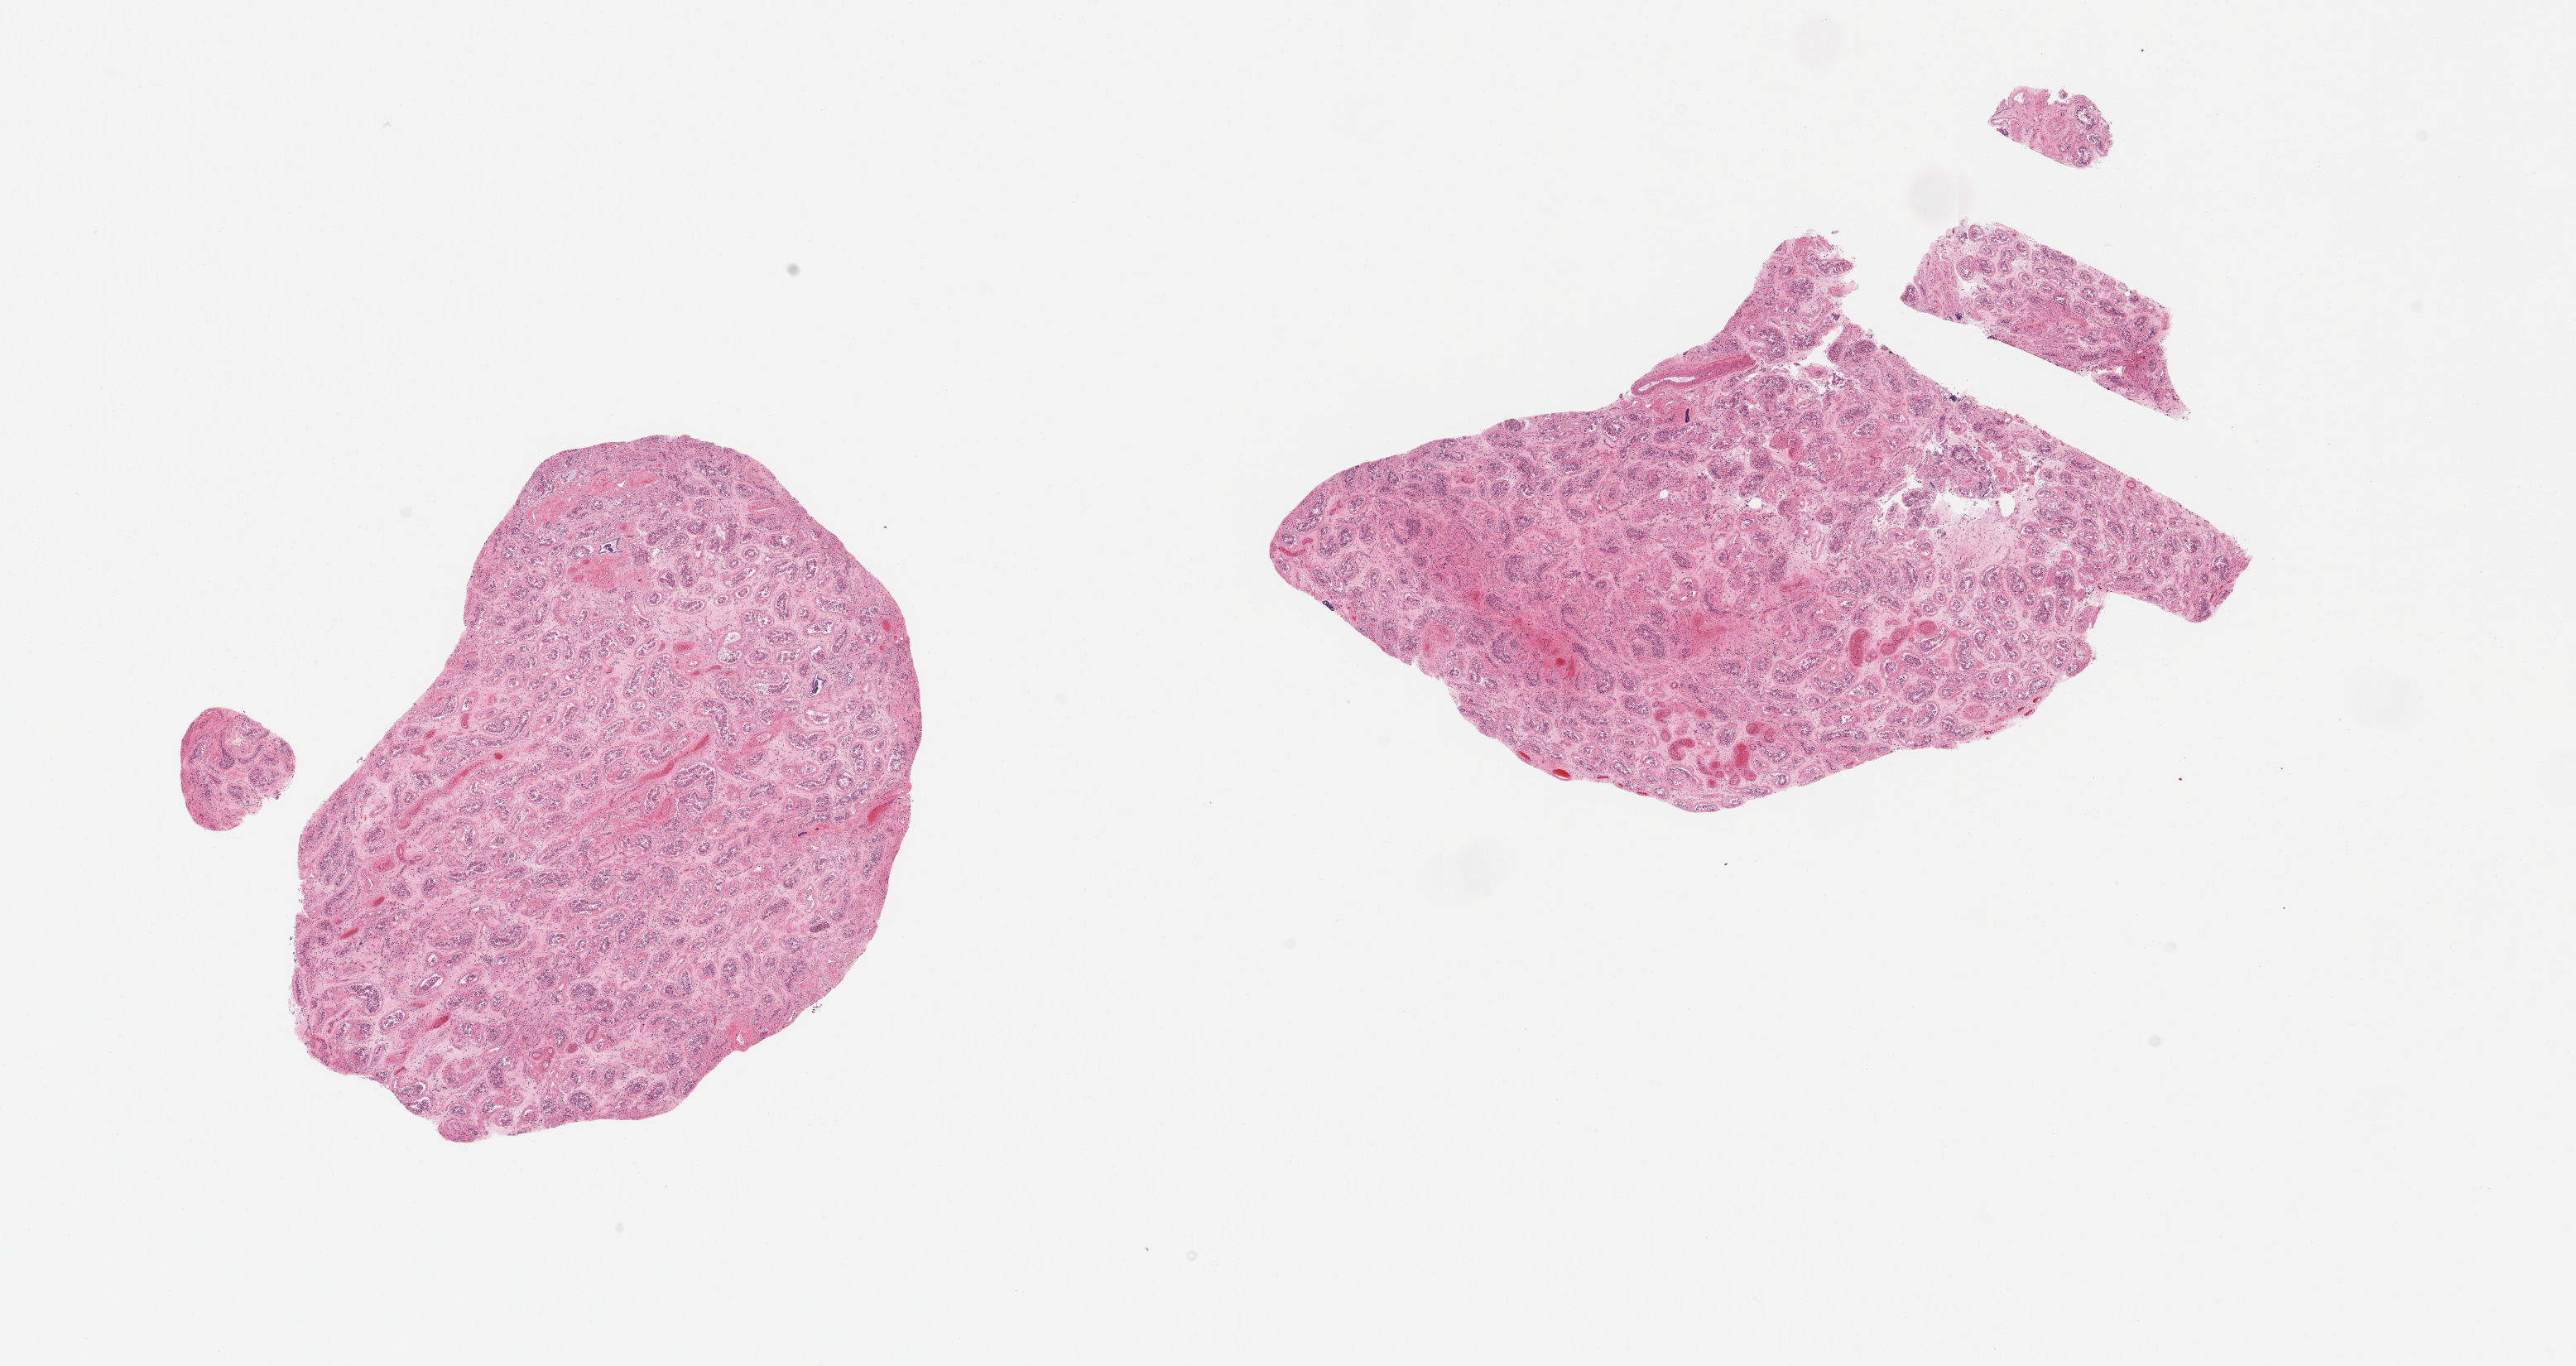
Haematoxylin and eosin whole-slide image — low-resolution overview of the scanned area, about 24.6 x 13.0 mm, PAXgene-fixed, paraffin-embedded tissue, section of testis (target tissue), tissue donor sample. Donor sex: male.
* review note (as recorded): 2 pieces, moderately advanced saponification. Islets not visible